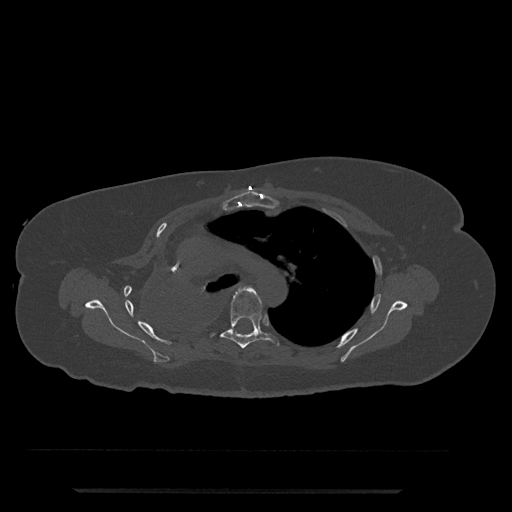
CT including the spine, one axial slice. Position 547 of 797 along the scan axis. 120 kVp. Bone window (W 1800 / L 400 HU). 0.5 mm slice thickness. 512 × 512 image matrix. Female patient, age 51 years. Case-level facts recorded for this patient, not image findings: primary cancer: neuro.
Structures marked on this image (semi-automatic segmentation, software-assisted and operator-edited):
- T5 vertebra: bounding box [x1, y1, x2, y2] px = [209, 287, 279, 349]